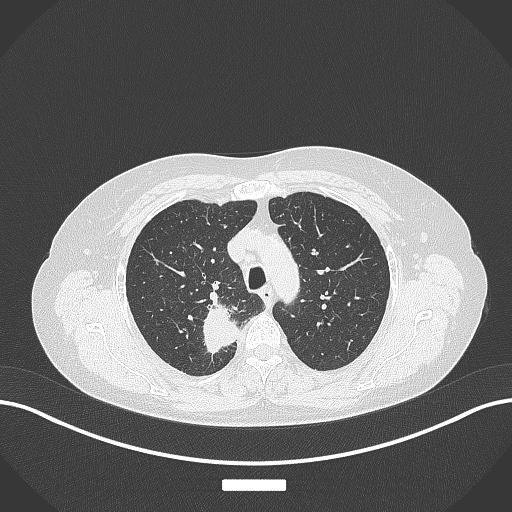
Chest CT, one axial slice; slice 293 of 357 in the series (ordered by position); reconstruction kernel B70f; 120 kVp; lung window (W 1500 / L -600 HU); 1 mm slice thickness; 512 × 512 image matrix, field of view 400 × 400 mm. Patient: female, 62 years. From the clinical record (not read from this slice): clinical TNM (as recorded): T1c N1 M0.
Structures marked on this image (rectangle marked by the reading radiologist):
- lung tumour (recorded histology: squamous cell carcinoma): bounding box <200,293,246,367> (left, top, right, bottom; pixels)